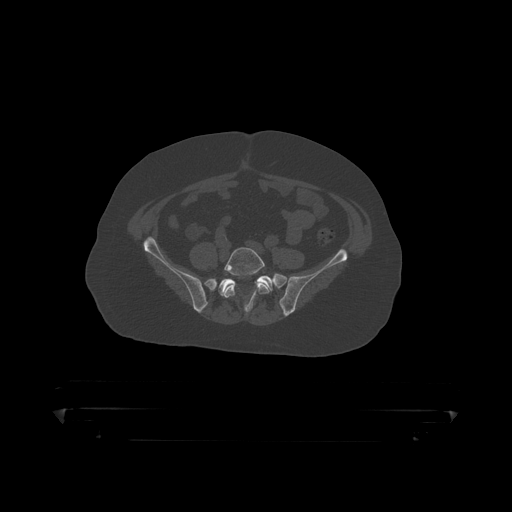
CT including the spine, one axial slice; slice 32 of 390 in the series (ordered by position); bone window (W 1800 / L 400 HU); 512 × 512 image matrix, field of view 650 × 650 mm. Patient: male, 60 years. Case-level facts recorded for this patient, not image findings: primary cancer: prostate.
Outlined on this slice (semi-automatic segmentation, software-assisted and operator-edited):
- L5 vertebra: bounding box <224,247,270,309> (left, top, right, bottom; pixels)